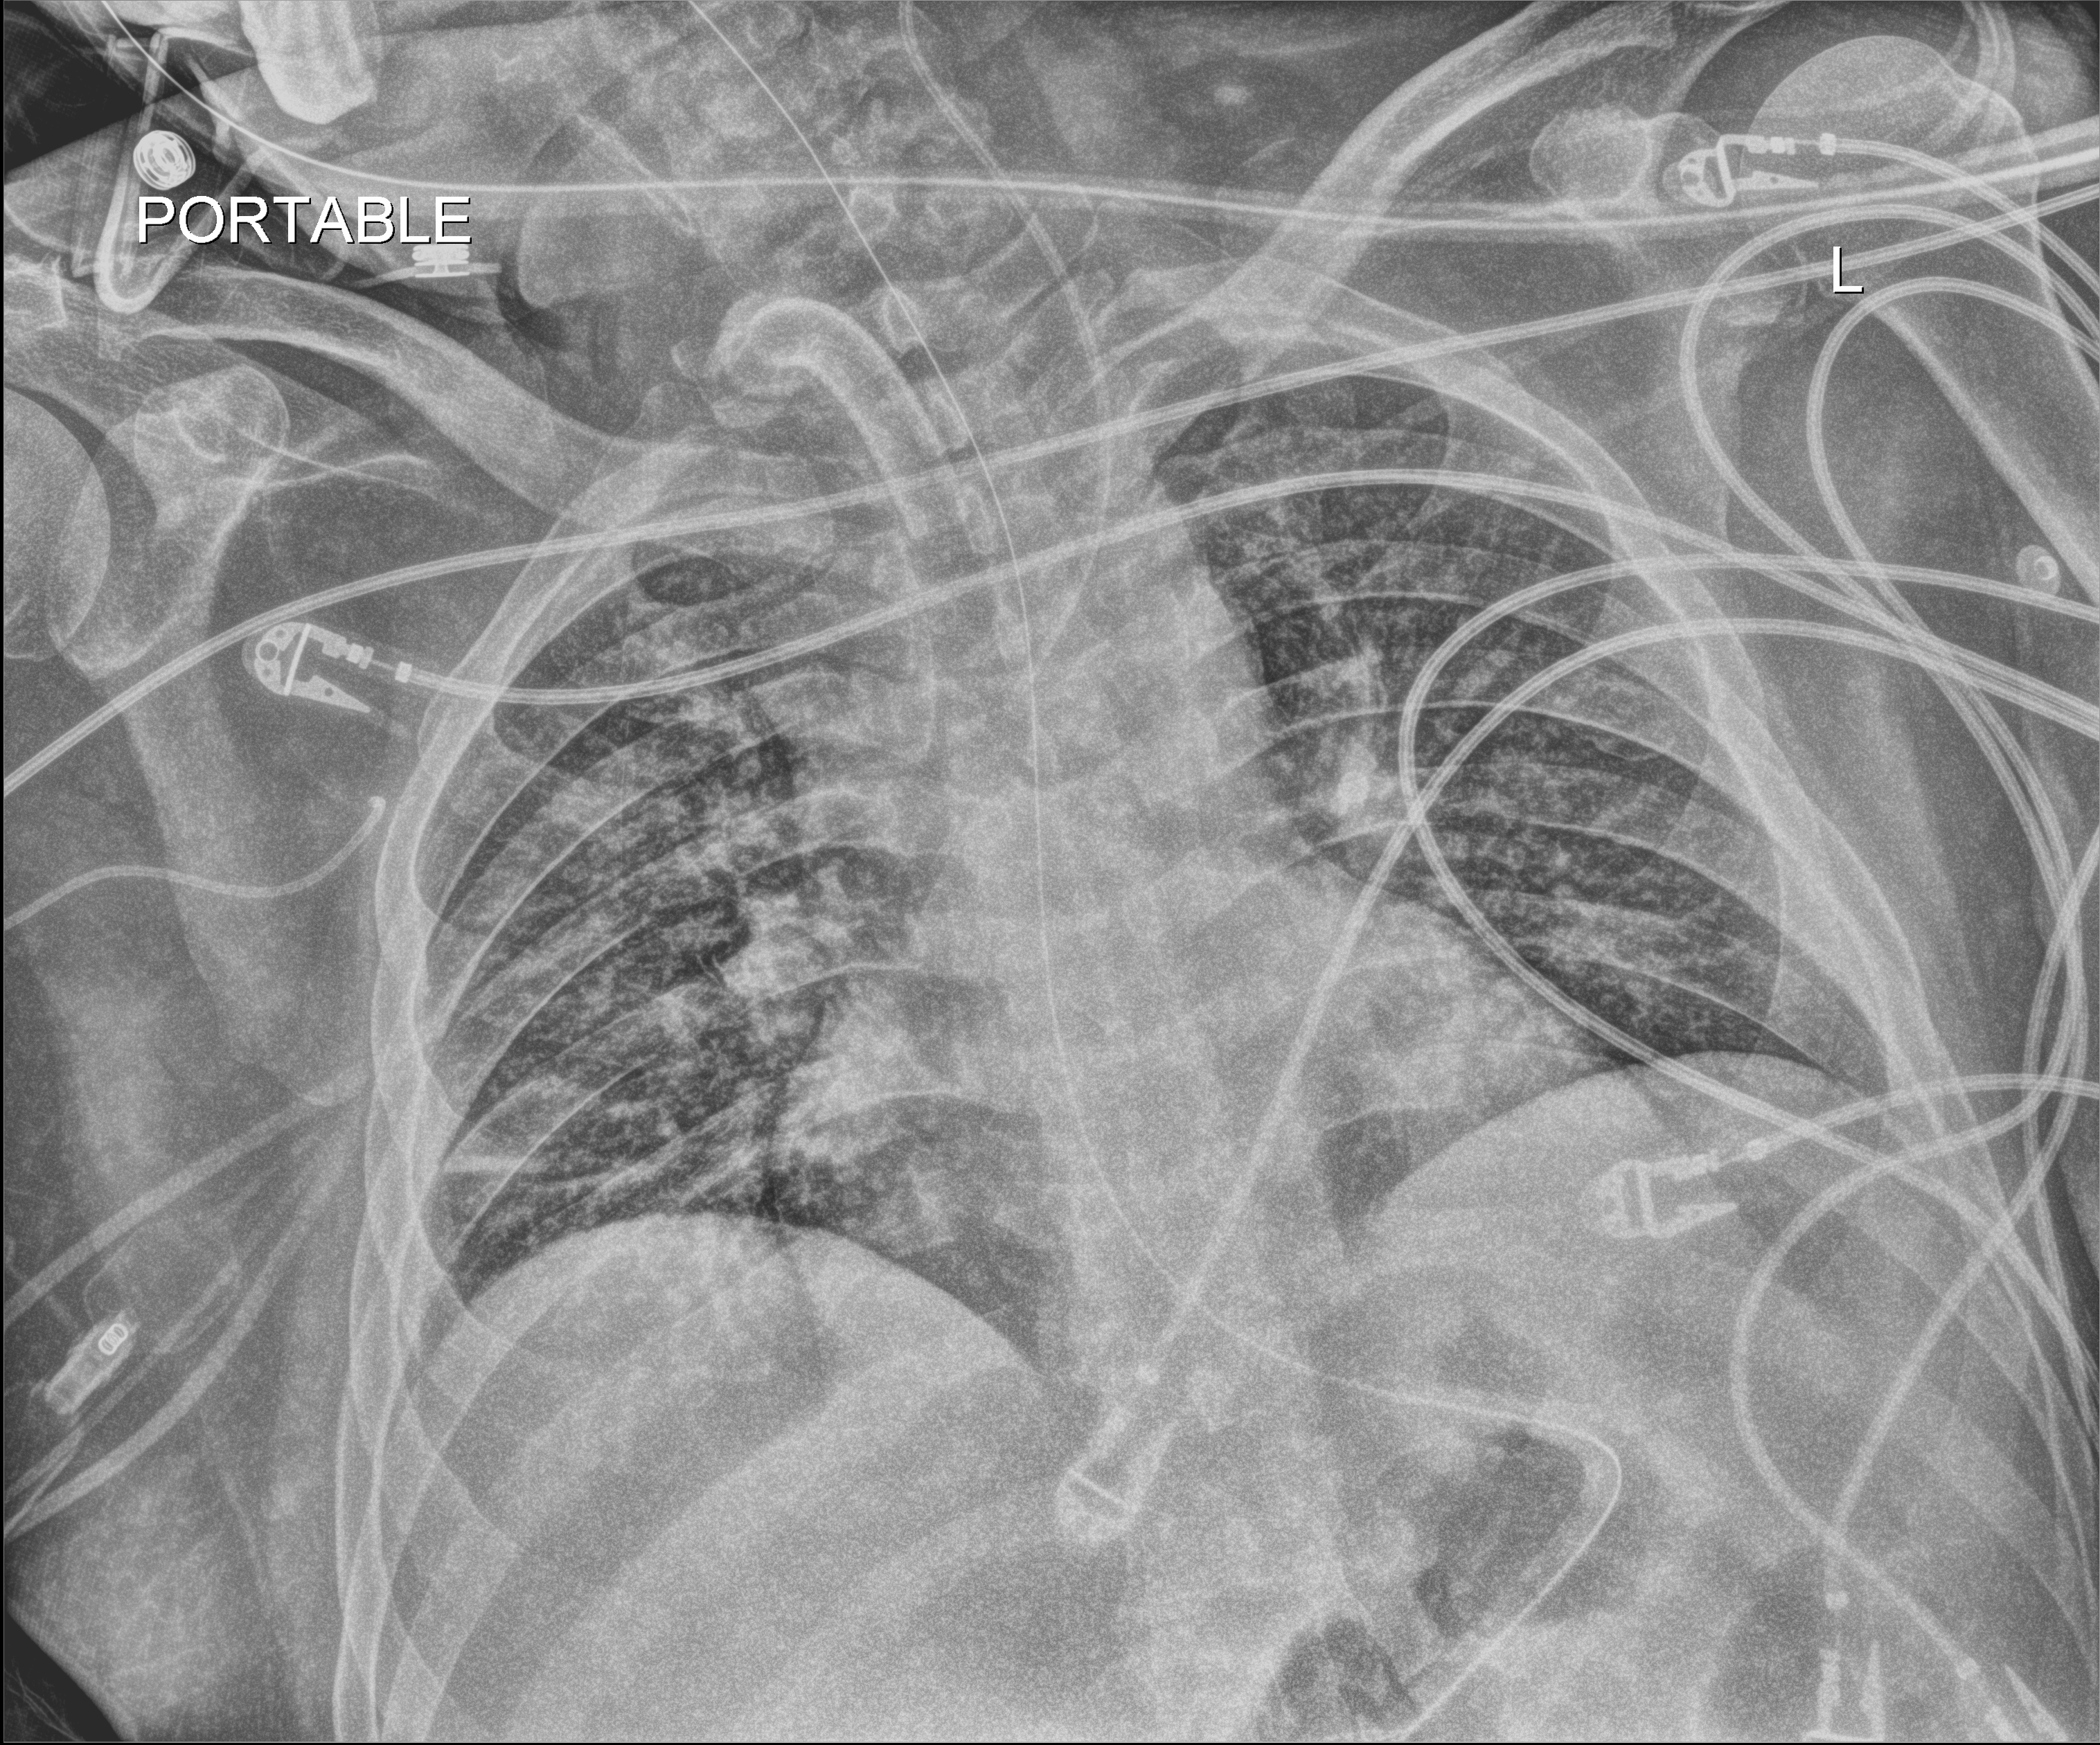
Bedside chest radiograph (digital radiography); anteroposterior (AP) projection. Male patient hospitalised with COVID-19, age 18–59 years.
Admission-level facts for this patient (not findings on this image; timing relative to this image not recorded): mechanically ventilated during this hospital stay: yes.